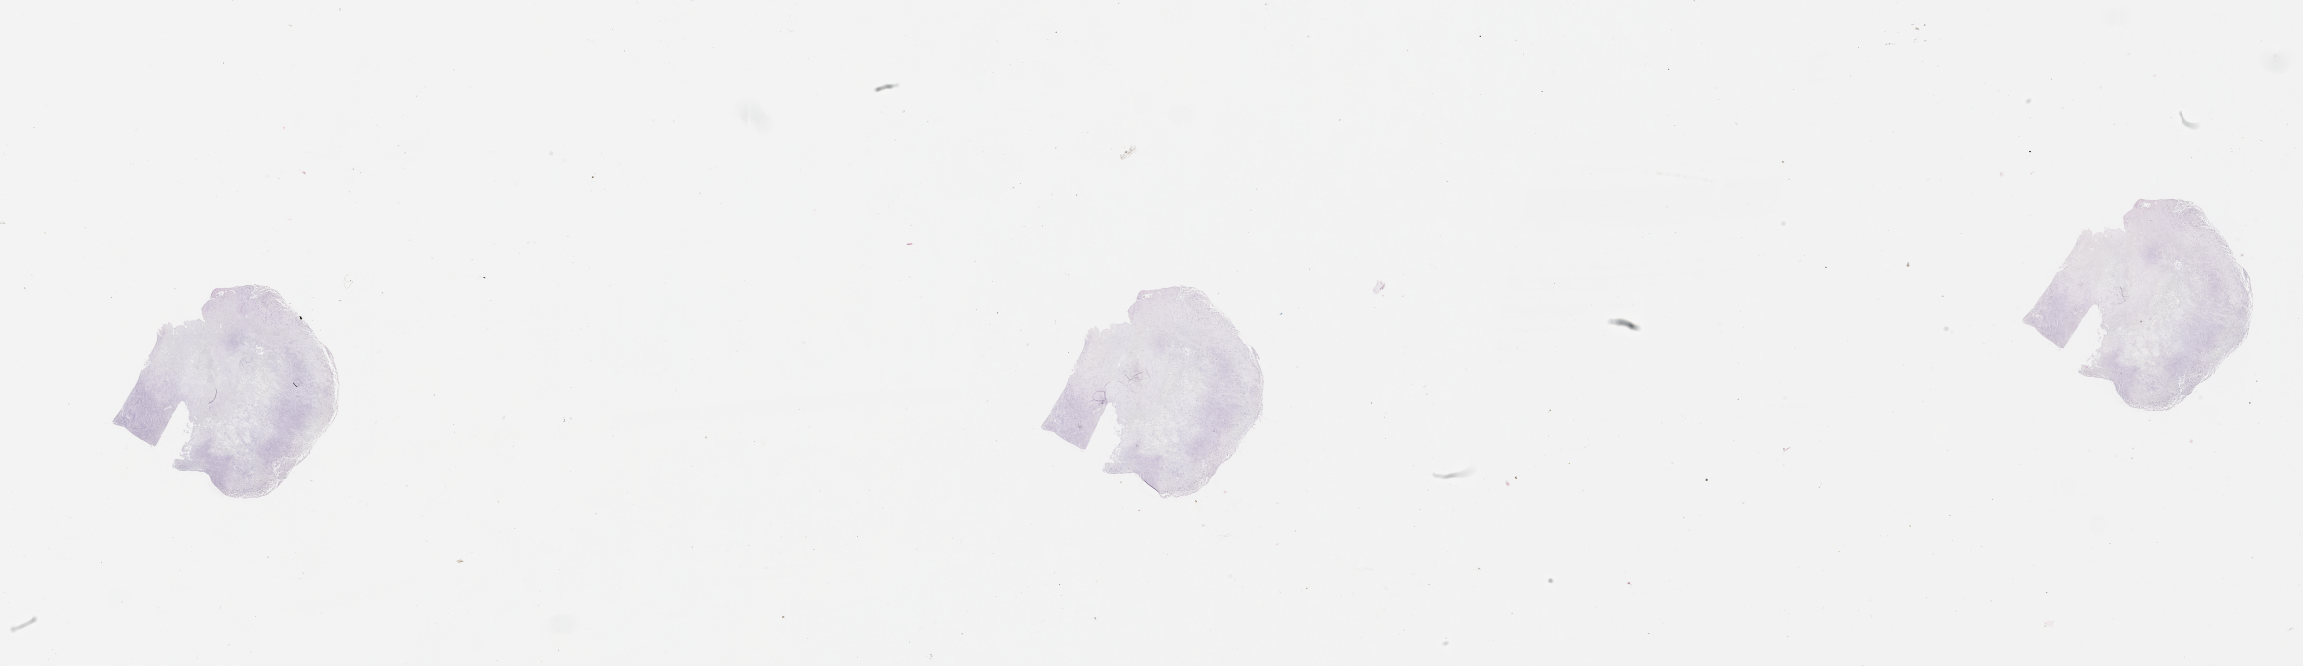
H&E-stained whole-slide image — whole scanned area (about 37.1 x 10.7 mm) shown as a low-resolution overview. Brain, tumour tissue. Patient: male, age 65 years.
* primary tumour site (as recorded): parietal lobe
* diagnosis: Glioblastoma